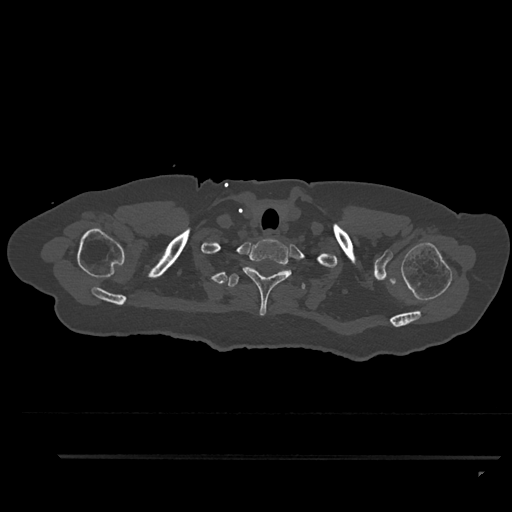
CT including the spine, one axial slice; slice 755 of 797 in the series (ordered by position); 120 kVp; bone window (W 1800 / L 400 HU); 512 × 512 image matrix, field of view 408 × 408 mm. Female patient, age 44 years. From the clinical record (not read from this slice): primary cancer: renal; vertebrae with lytic lesions (as recorded): L1.
Structures marked on this image (semi-automatically segmented with operator editing):
- T1 vertebra: box from (x=242, y=238) to (x=292, y=316) px
- T2 vertebra: (x=228, y=273)–(x=305, y=289)